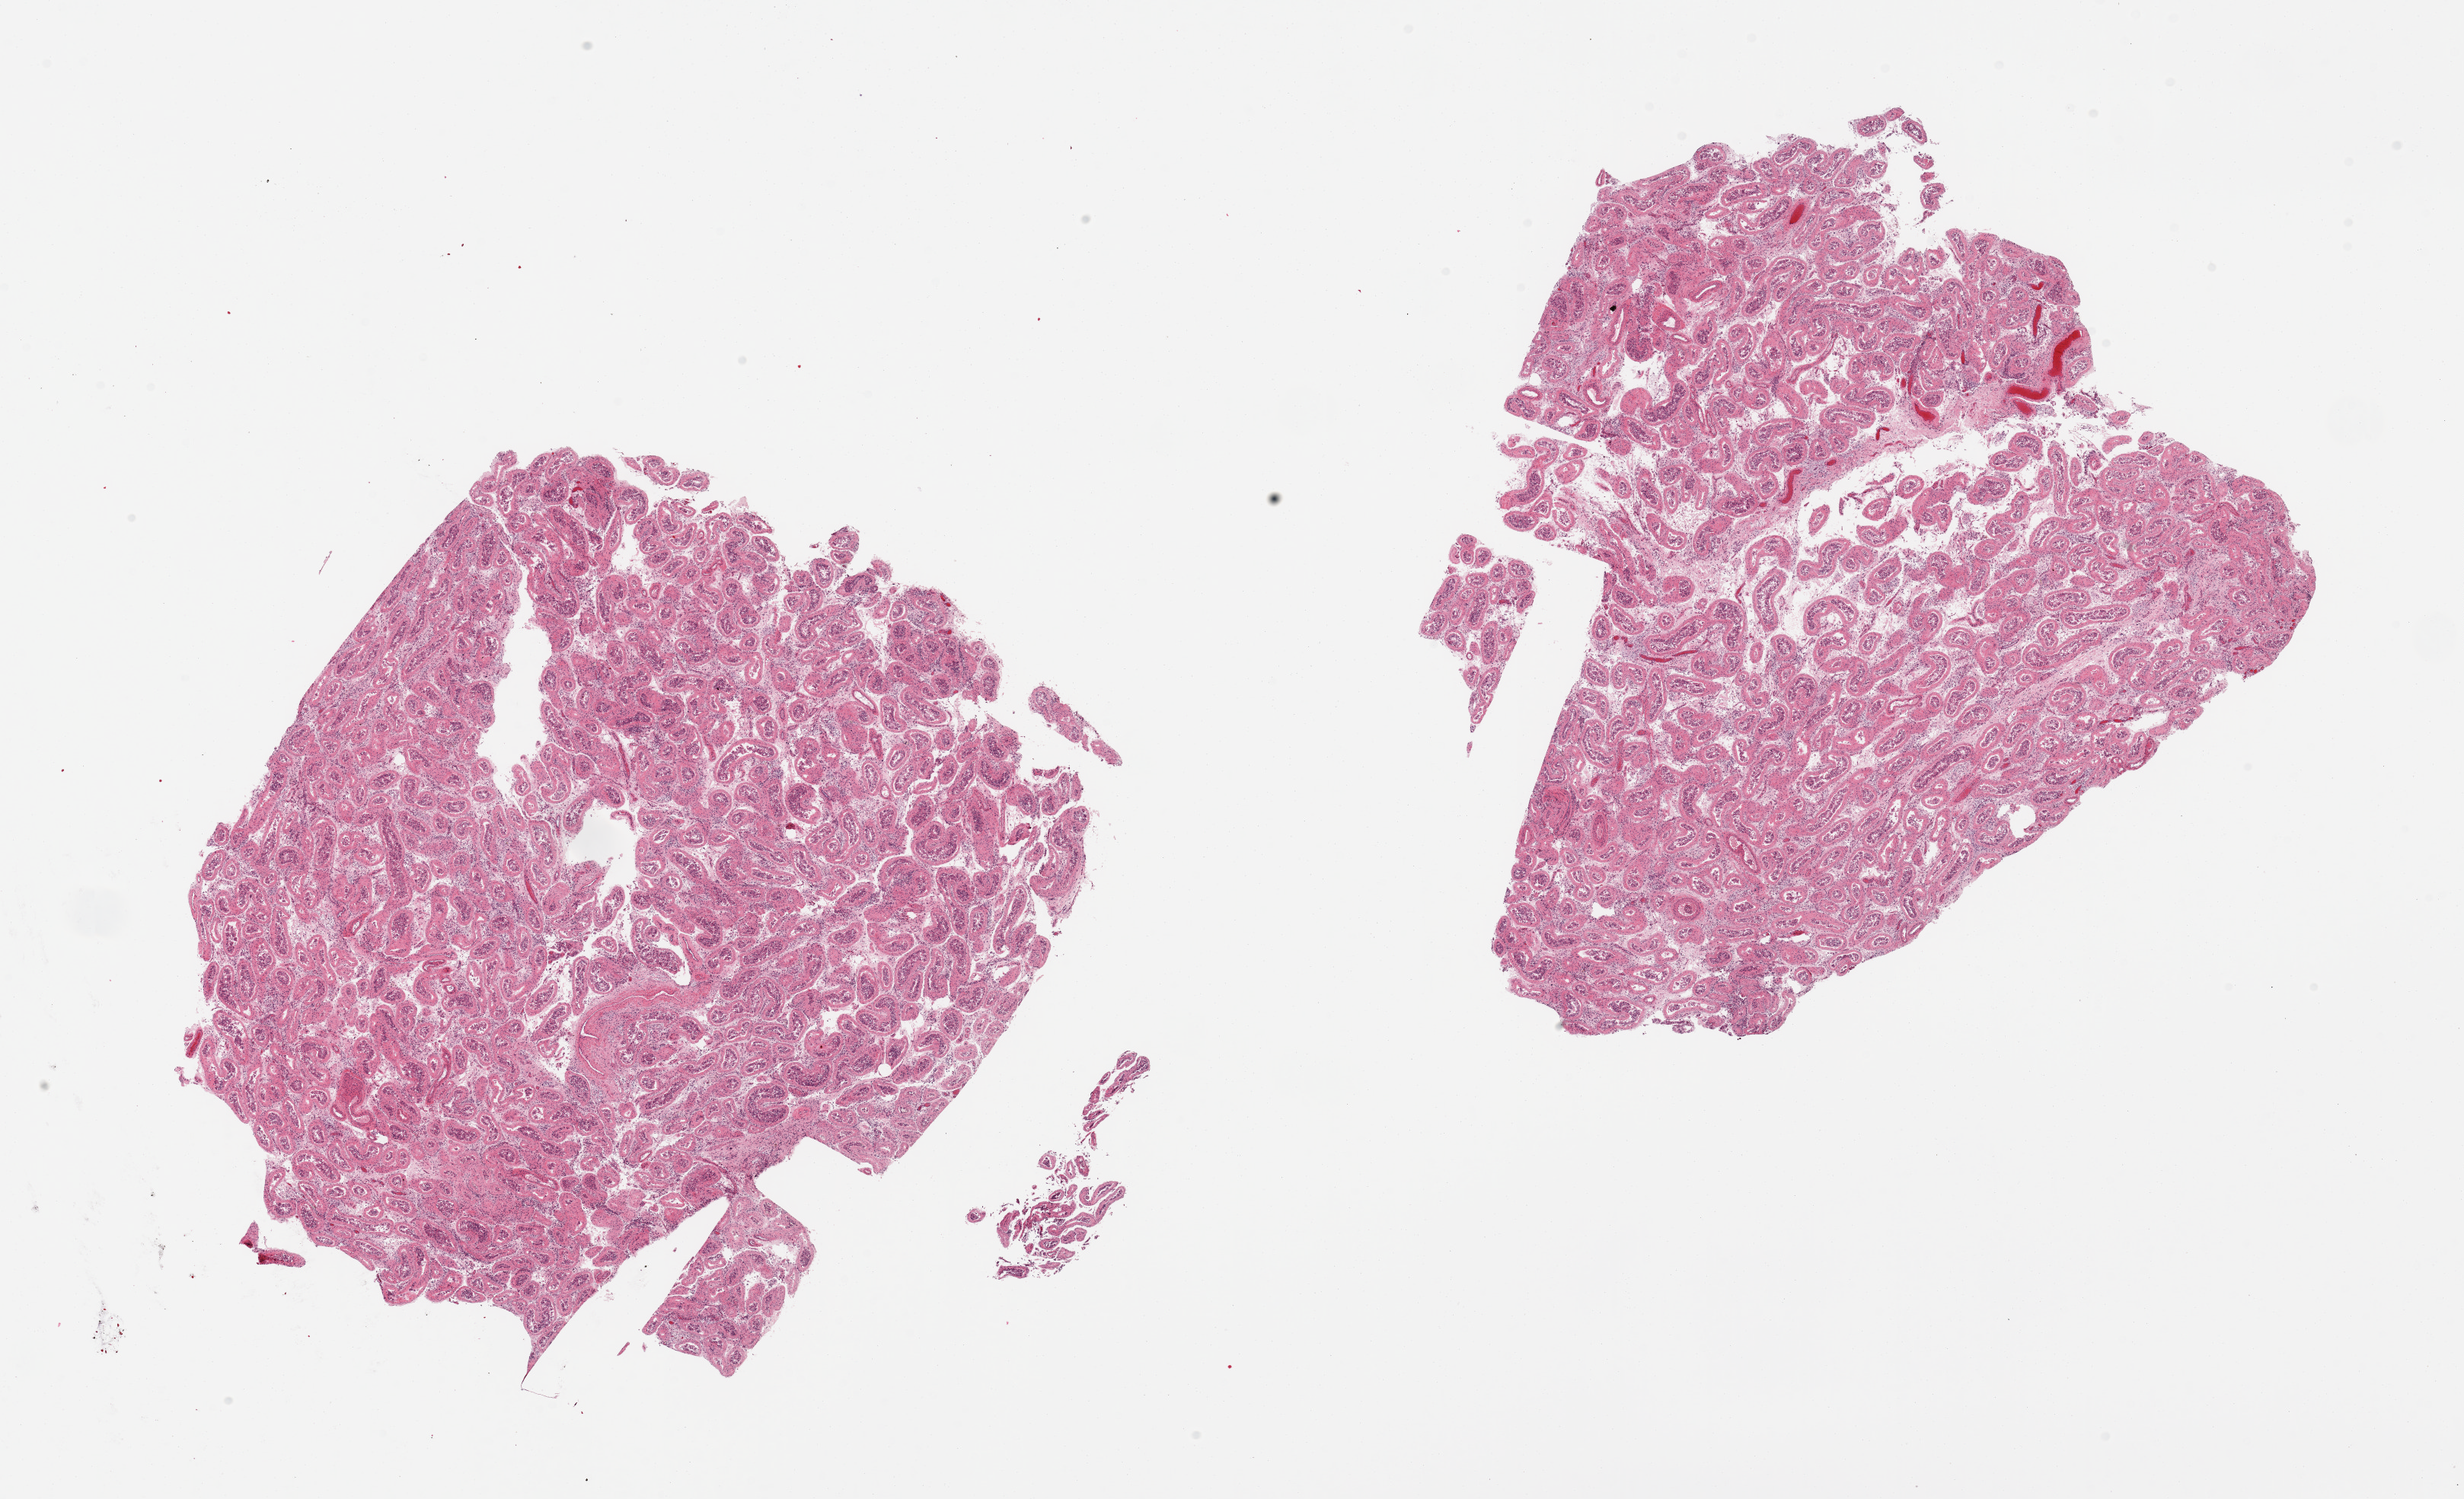
Digitized hematoxylin and eosin (H&E)-stained section, a low-resolution overview of the entire scanned area, about 25.6 x 15.6 mm (slide scanned at 20x); PAXgene-fixed paraffin-embedded (PFPE) section; section of testis (target tissue); donor tissue sample. Donor sex: male.
Review note (as recorded): 2 pieces, moderately advance autolysis, unable to assess spermatogenesis.